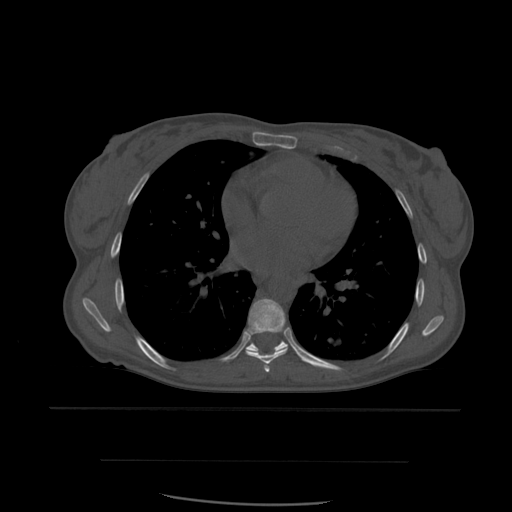
CT including the spine, one axial slice. Position 368 of 574 along the scan axis. Bone window (W 1800 / L 400 HU). 1.25 mm slice thickness. 512 × 512 image matrix. Patient age 48 years. From the clinical record (not read from this slice): primary cancer: lung.
Structures marked on this image (semi-automatic segmentation, software-assisted and operator-edited):
- T6 vertebra: bounding box (x1, y1, x2, y2) in pixels: (265, 367, 270, 372)
- T7 vertebra: (246, 299, 288, 372)
- T8 vertebra: (247, 341, 288, 353)